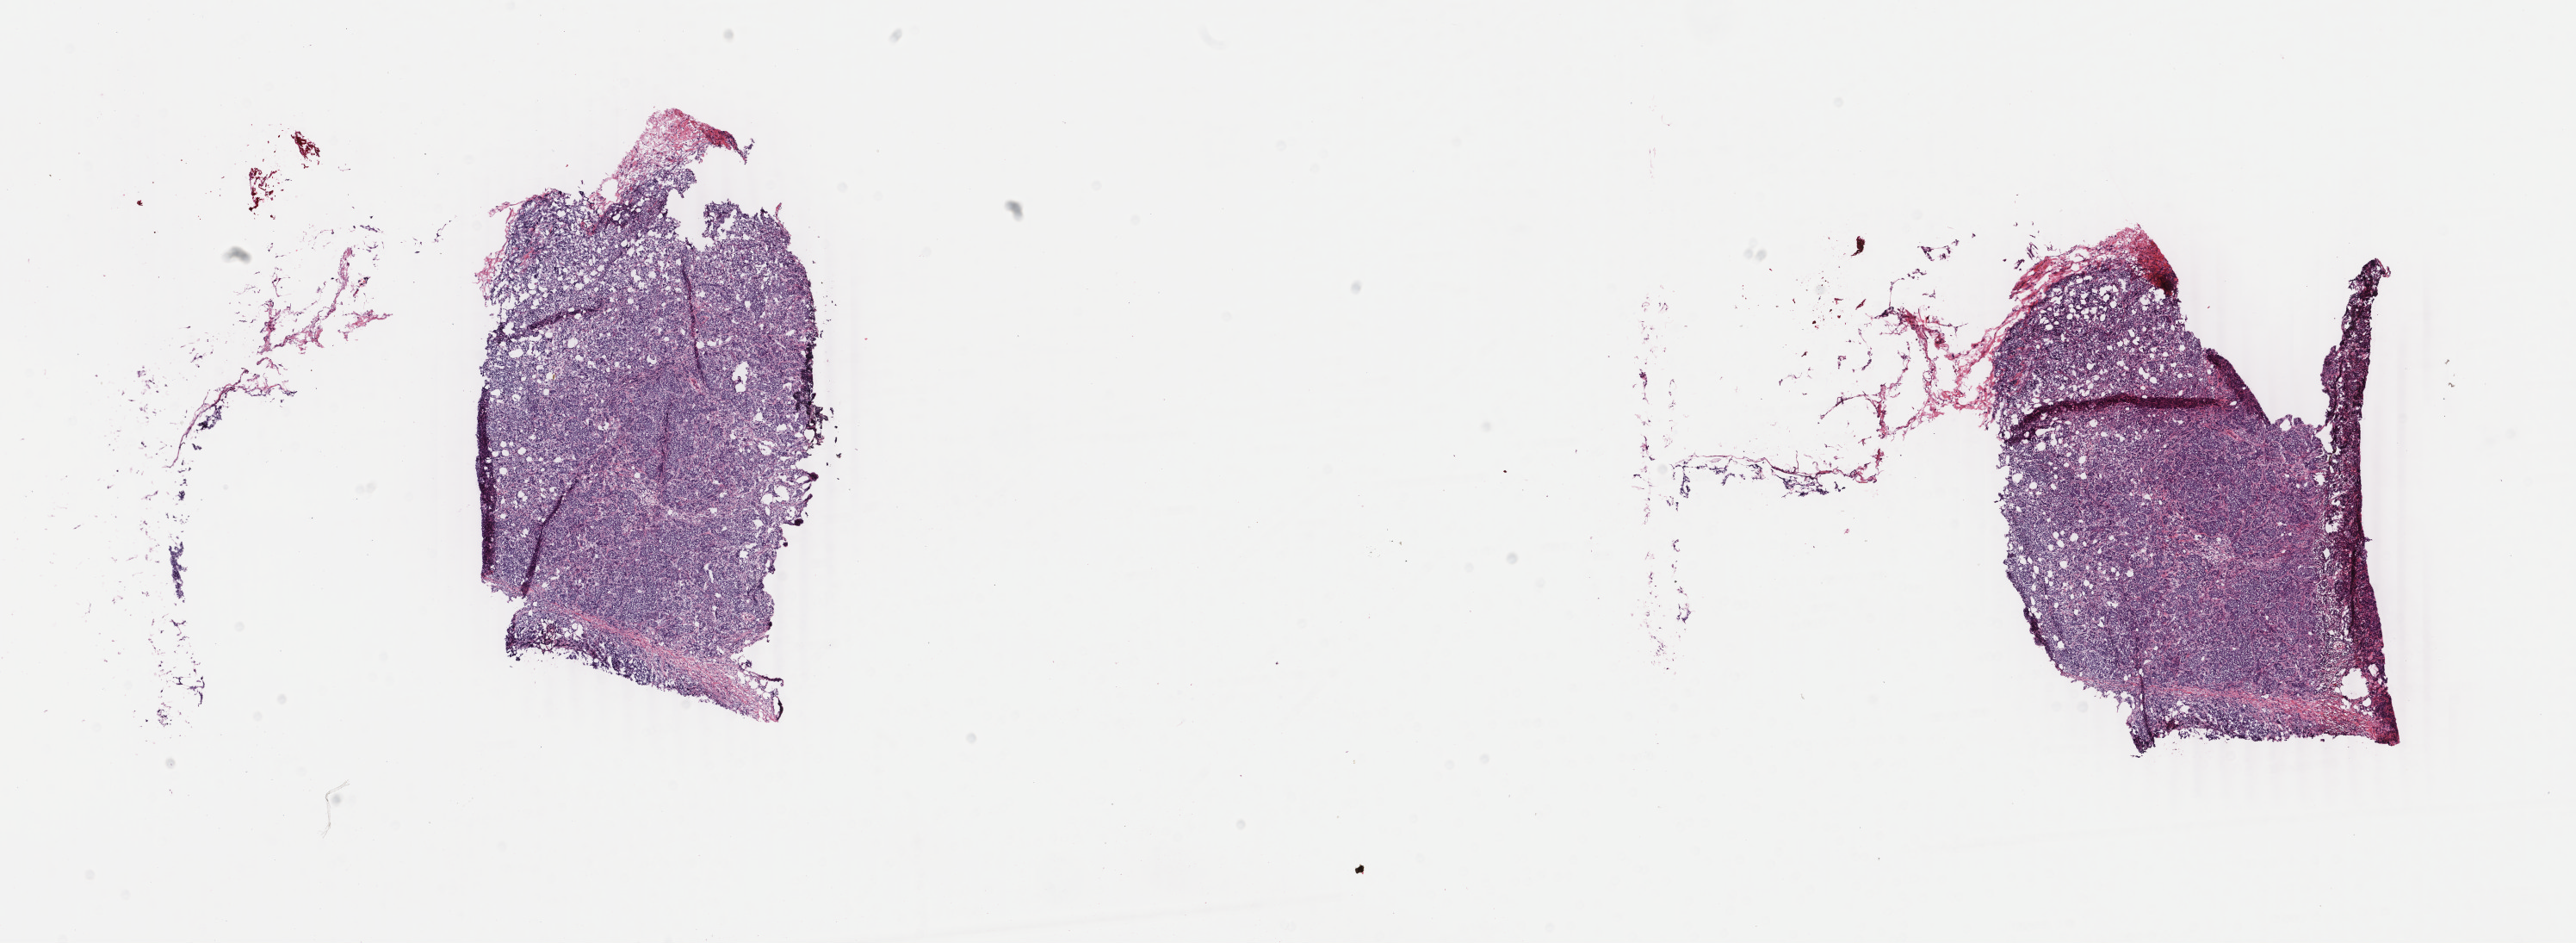
H&E whole-slide image, a low-resolution overview of the entire scanned area, about 23.8 x 8.7 mm (slide scanned at 40x). Frozen section. Primary tumour sample from the breast. Female patient; age at initial diagnosis 82 years. Slide review estimates, as recorded: tumour cells 90%, tumour nuclei 95%, normal cells 0%, stromal cells 10%, necrosis 0%. Infiltration values recorded for this section: lymphocyte infiltration 1%, monocyte infiltration 0%, neutrophil infiltration 0%.
AJCC pathologic stage: IV. Histologic diagnosis: Infiltrating duct carcinoma, NOS. Lymph nodes positive (case pathology): 4 of 15 examined.